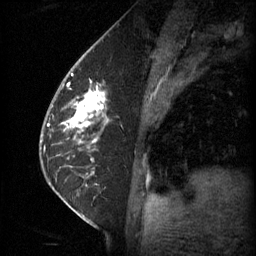
Breast MRI (dynamic contrast-enhanced), one sagittal slice; slice 26 of 60 in the series (ordered by position); 3 images stored at this slice position (order not interpretable as contrast timing); 1.5 T; TE 4.2 ms, TR 11 ms; 2 mm slice thickness; 256 × 256 image matrix, field of view 180 × 180 mm. Female patient, age 62 years.
Structures marked on this image (semi-automatic segmentation, software-assisted and operator-edited):
- analysis volume of interest (the breast-tissue region the enhancement analysis was run in; not a lesion): box from (x=55, y=72) to (x=111, y=133) px
- tumour enhancement mask (voxels above the 70 % enhancement threshold inside the analysis volume of interest): (x=65, y=86)–(x=106, y=131)